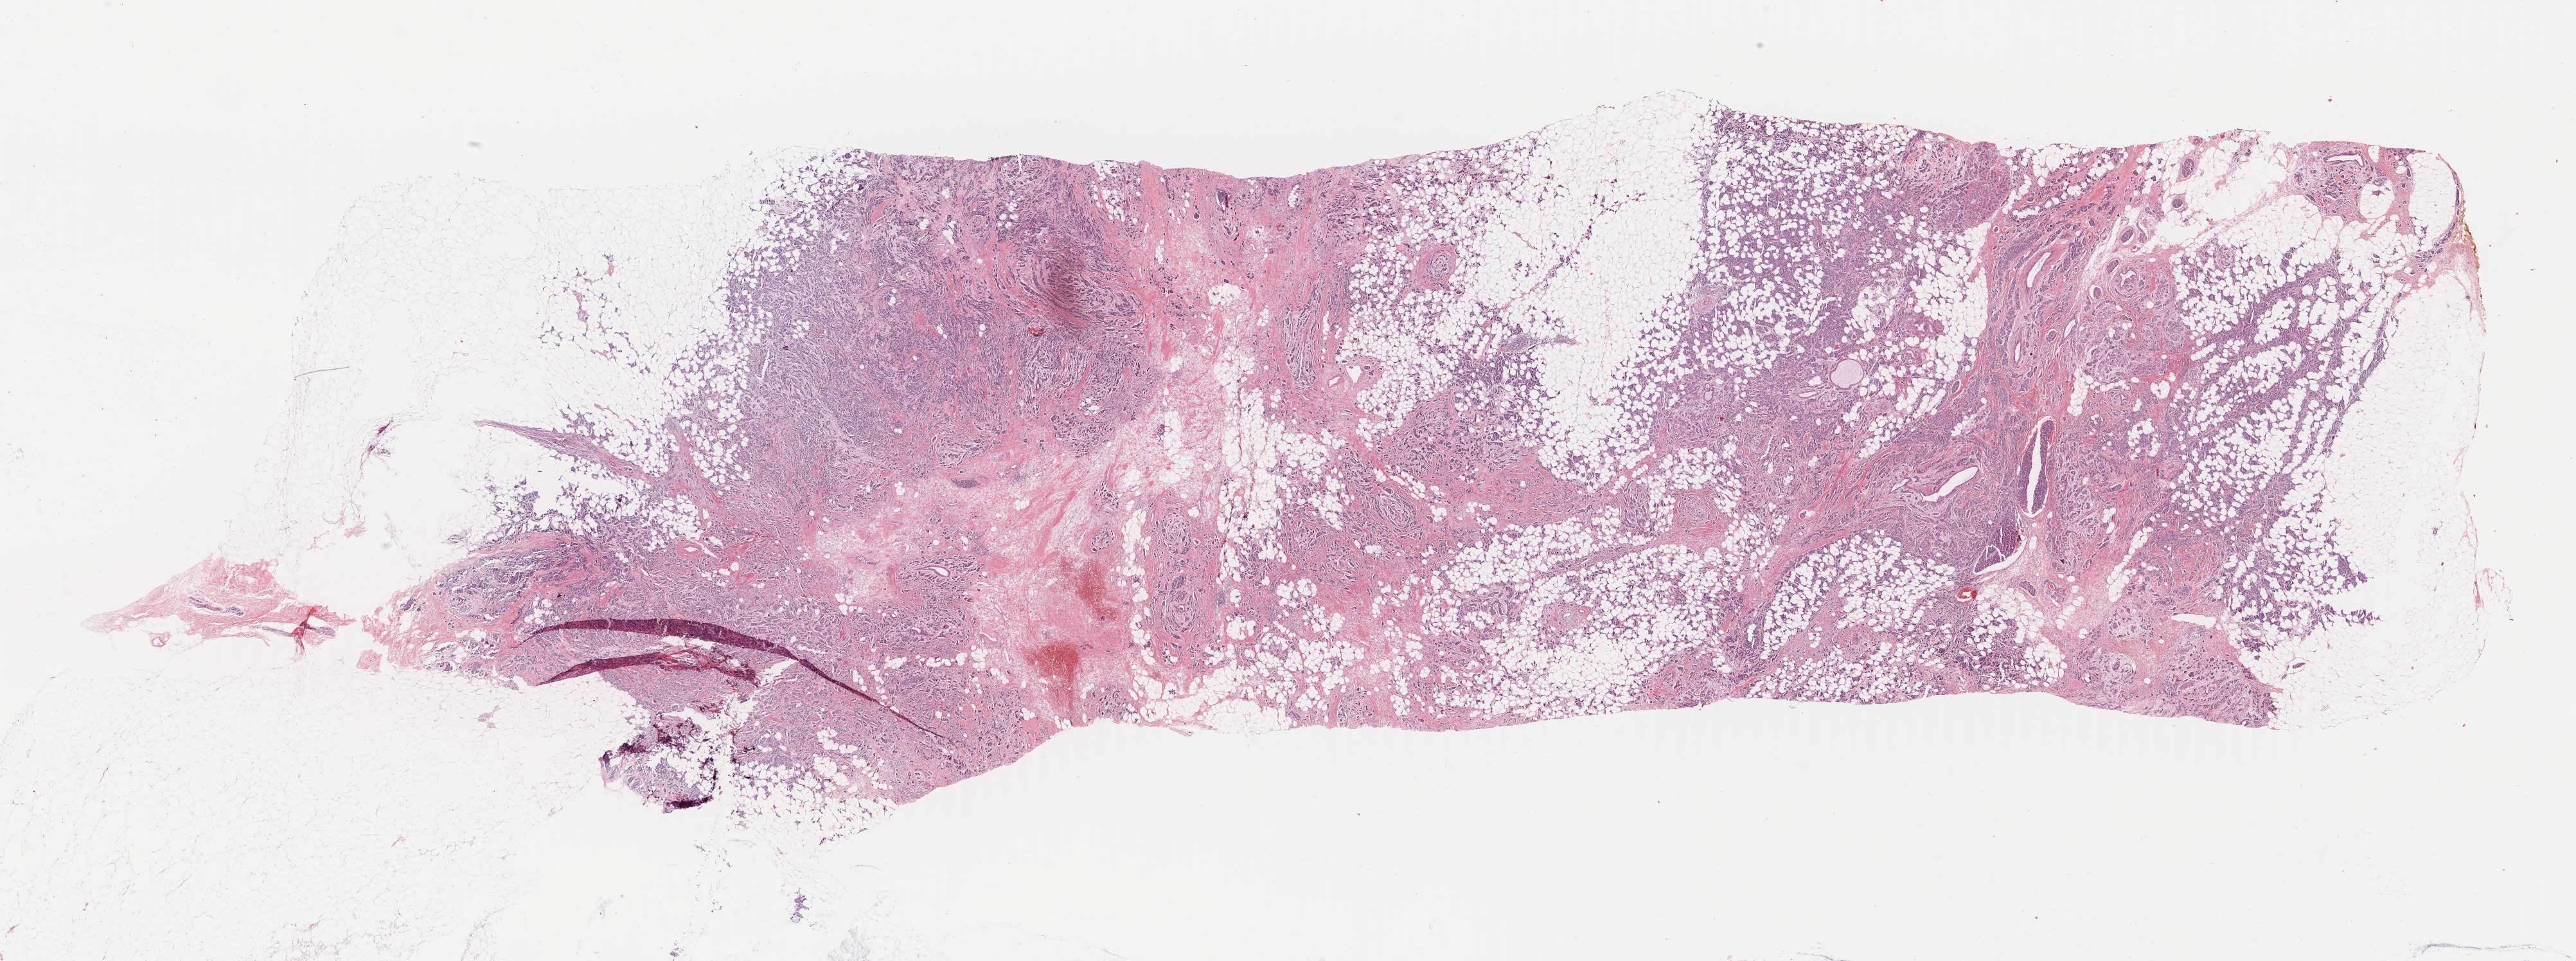
Digitized H&E tissue section (whole slide) — shown as a low-resolution overview of the whole scanned area (about 31.9 x 11.9 mm), formalin-fixed paraffin-embedded (FFPE) diagnostic section, primary tumour sample from the breast. Female, age 62 years at initial diagnosis.
Laterality: right. Diagnosis: Infiltrating duct carcinoma, NOS. AJCC pathologic stage: IIIA.